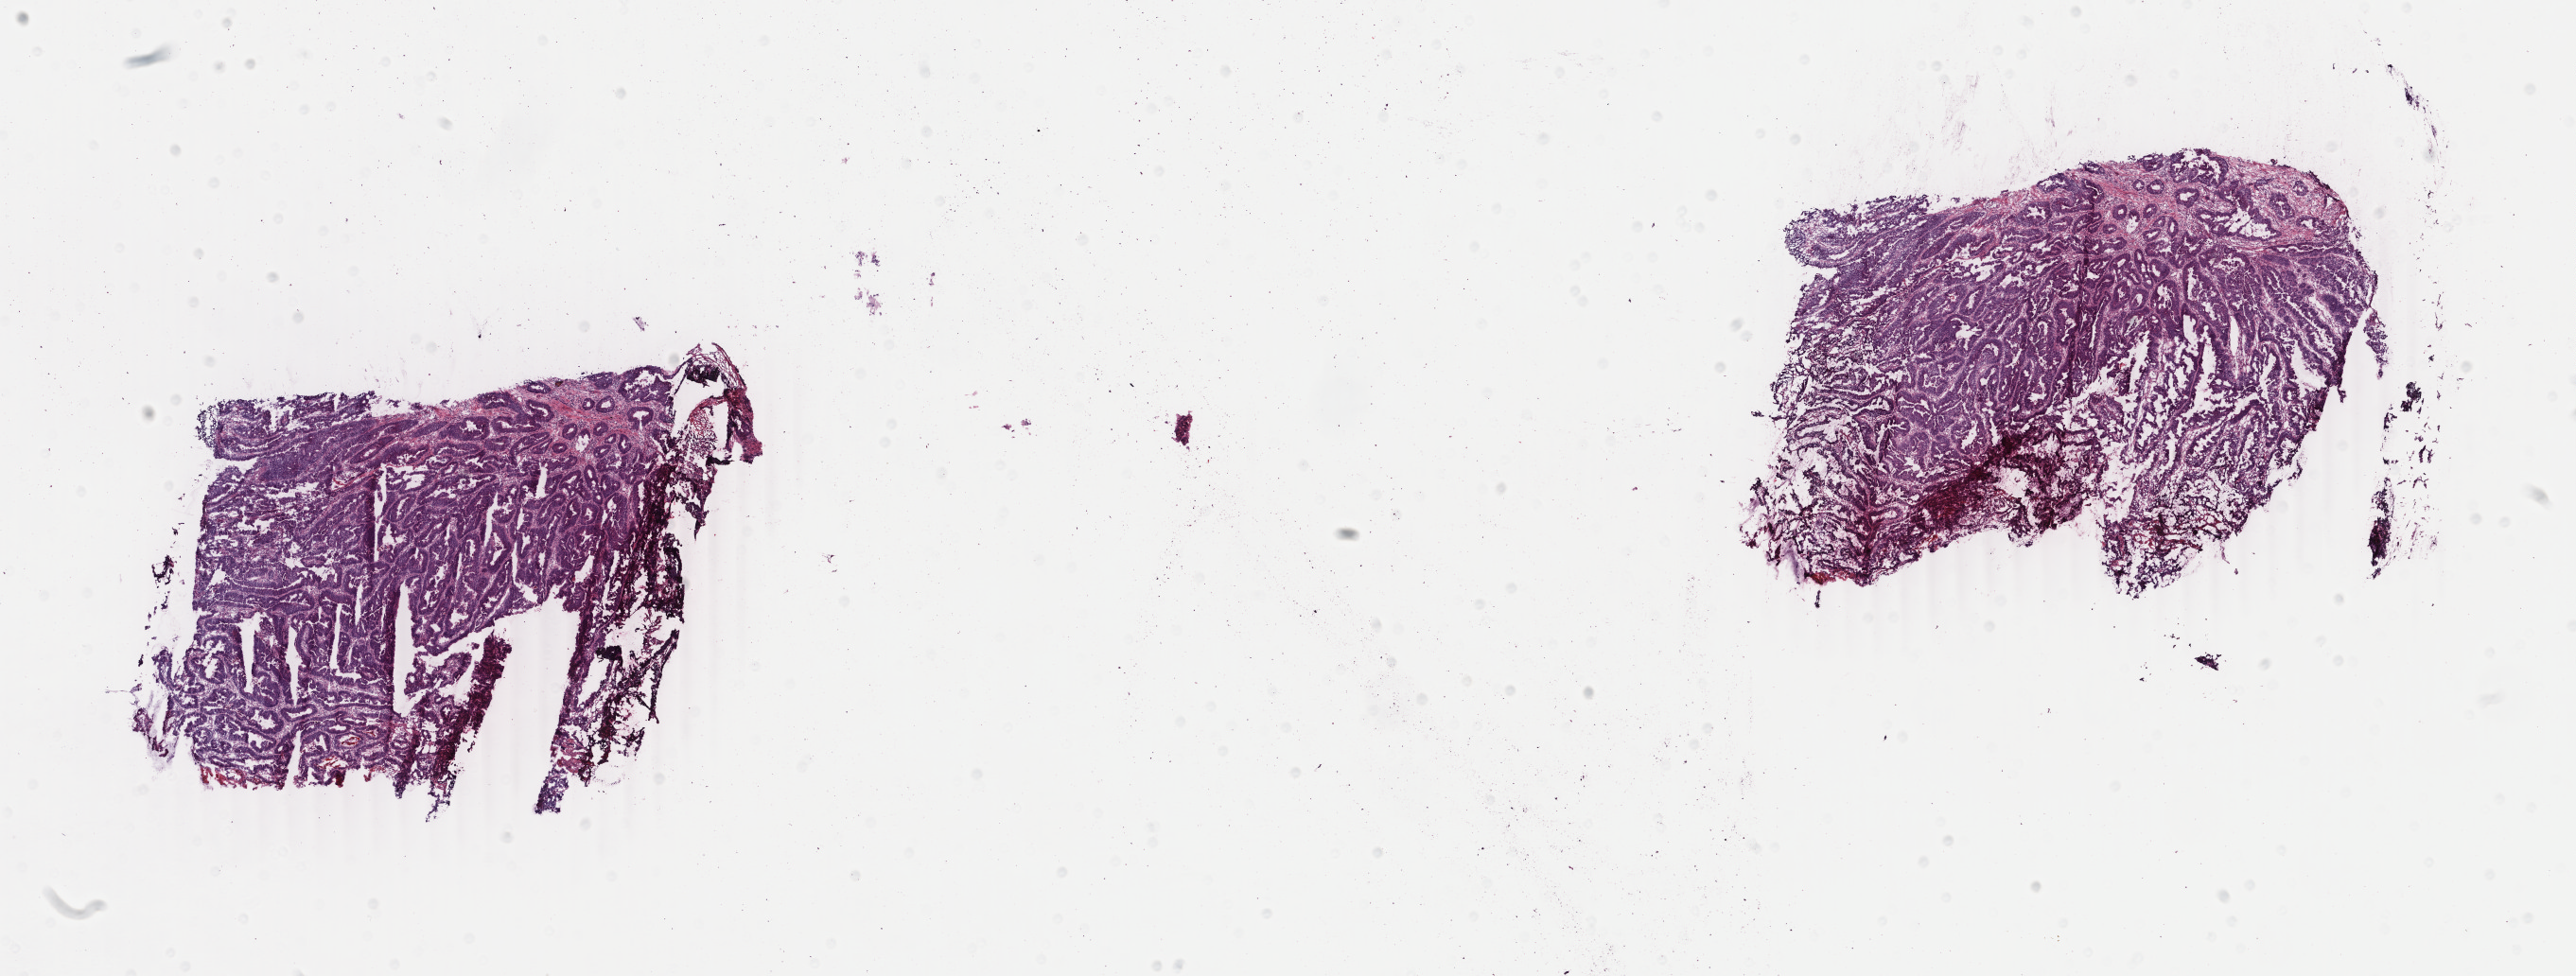
H&E-stained whole-slide image, shown as a low-resolution overview of the whole scanned area (about 21.7 x 8.2 mm), frozen section from the top of the tissue portion, sample: primary tumour, rectum. Patient: male, age at initial diagnosis 66 years. Slide review estimates, as recorded: tumour cells 68%, tumour nuclei 75%, normal cells 10%, stromal cells 20%, necrosis 2%. Inflammatory infiltration, as recorded: lymphocyte infiltration 12%, monocyte infiltration 1%, neutrophil infiltration 4%.
- pathologic diagnosis: Adenocarcinoma, NOS
- TNM: T4 N0 M0
- AJCC pathologic stage: II (5th edition)
- lymph nodes positive (case pathology): 0 of 15 examined